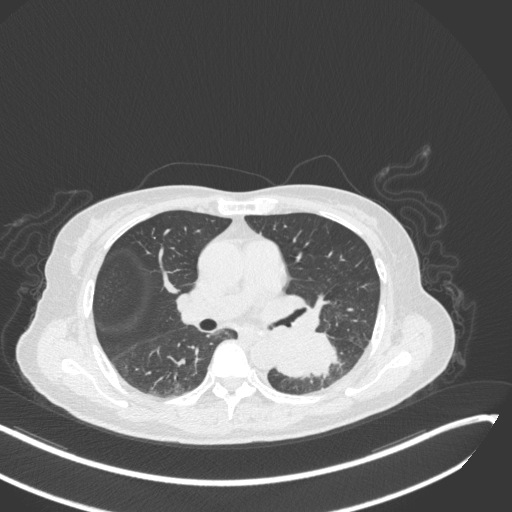
Chest CT, one axial slice; position 156 of 342 along the scan axis; reconstruction kernel B31f; lung window (W 1500 / L -600 HU); 1 mm slice thickness; 512 × 512 image matrix. Female patient, age 64 years. From the clinical record (not read from this slice): clinical TNM (as recorded): T3 N1 M1; histopathological grade: G3.
Structures marked on this image (rectangle marked by the reading radiologist):
- lung tumour (recorded histology: small cell carcinoma): bounding box <275,329,343,382> (left, top, right, bottom; pixels)